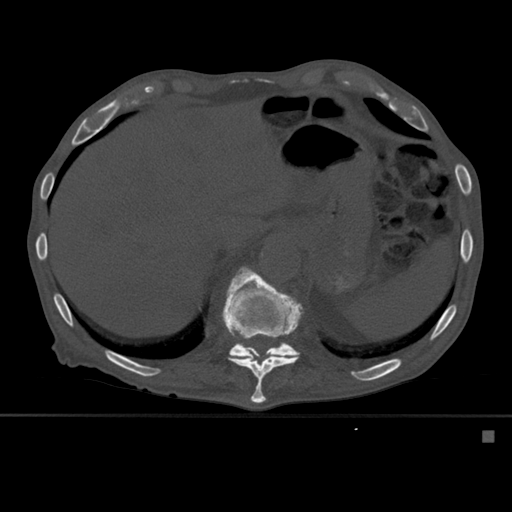
CT including the spine, one axial slice; position 288 of 527 along the scan axis; bone window (W 1800 / L 400 HU); 1.5 mm slice thickness; 512 × 512 image matrix, field of view 373 × 373 mm. Patient: male, 78 years. Case-level facts recorded for this patient, not image findings: primary cancer: prostate.
Annotated regions visible in this slice (semi-automatic segmentation, software-assisted and operator-edited):
- T11 vertebra: box from (x=222, y=267) to (x=304, y=404) px
- T12 vertebra: (x=229, y=280)–(x=300, y=358)